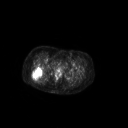
FDG PET of an extremity soft-tissue mass (from a PET/CT study), one axial slice; slice 57 of 267 in the series (ordered by position); 3.27 mm slice thickness; 128 × 128 image matrix. Patient: female, 70 years. From the clinical record (not read from this slice): histological type: synovial sarcoma; grade: intermediate; site of the primary tumour: right buttock.
Annotated regions visible in this slice (expert contour drawn on MRI and transferred to this co-registered scan by the dataset authors):
- gross tumour volume including surrounding oedema: box from (x=32, y=66) to (x=44, y=81) px
- gross tumour volume (mass): (x=32, y=66)–(x=44, y=79)